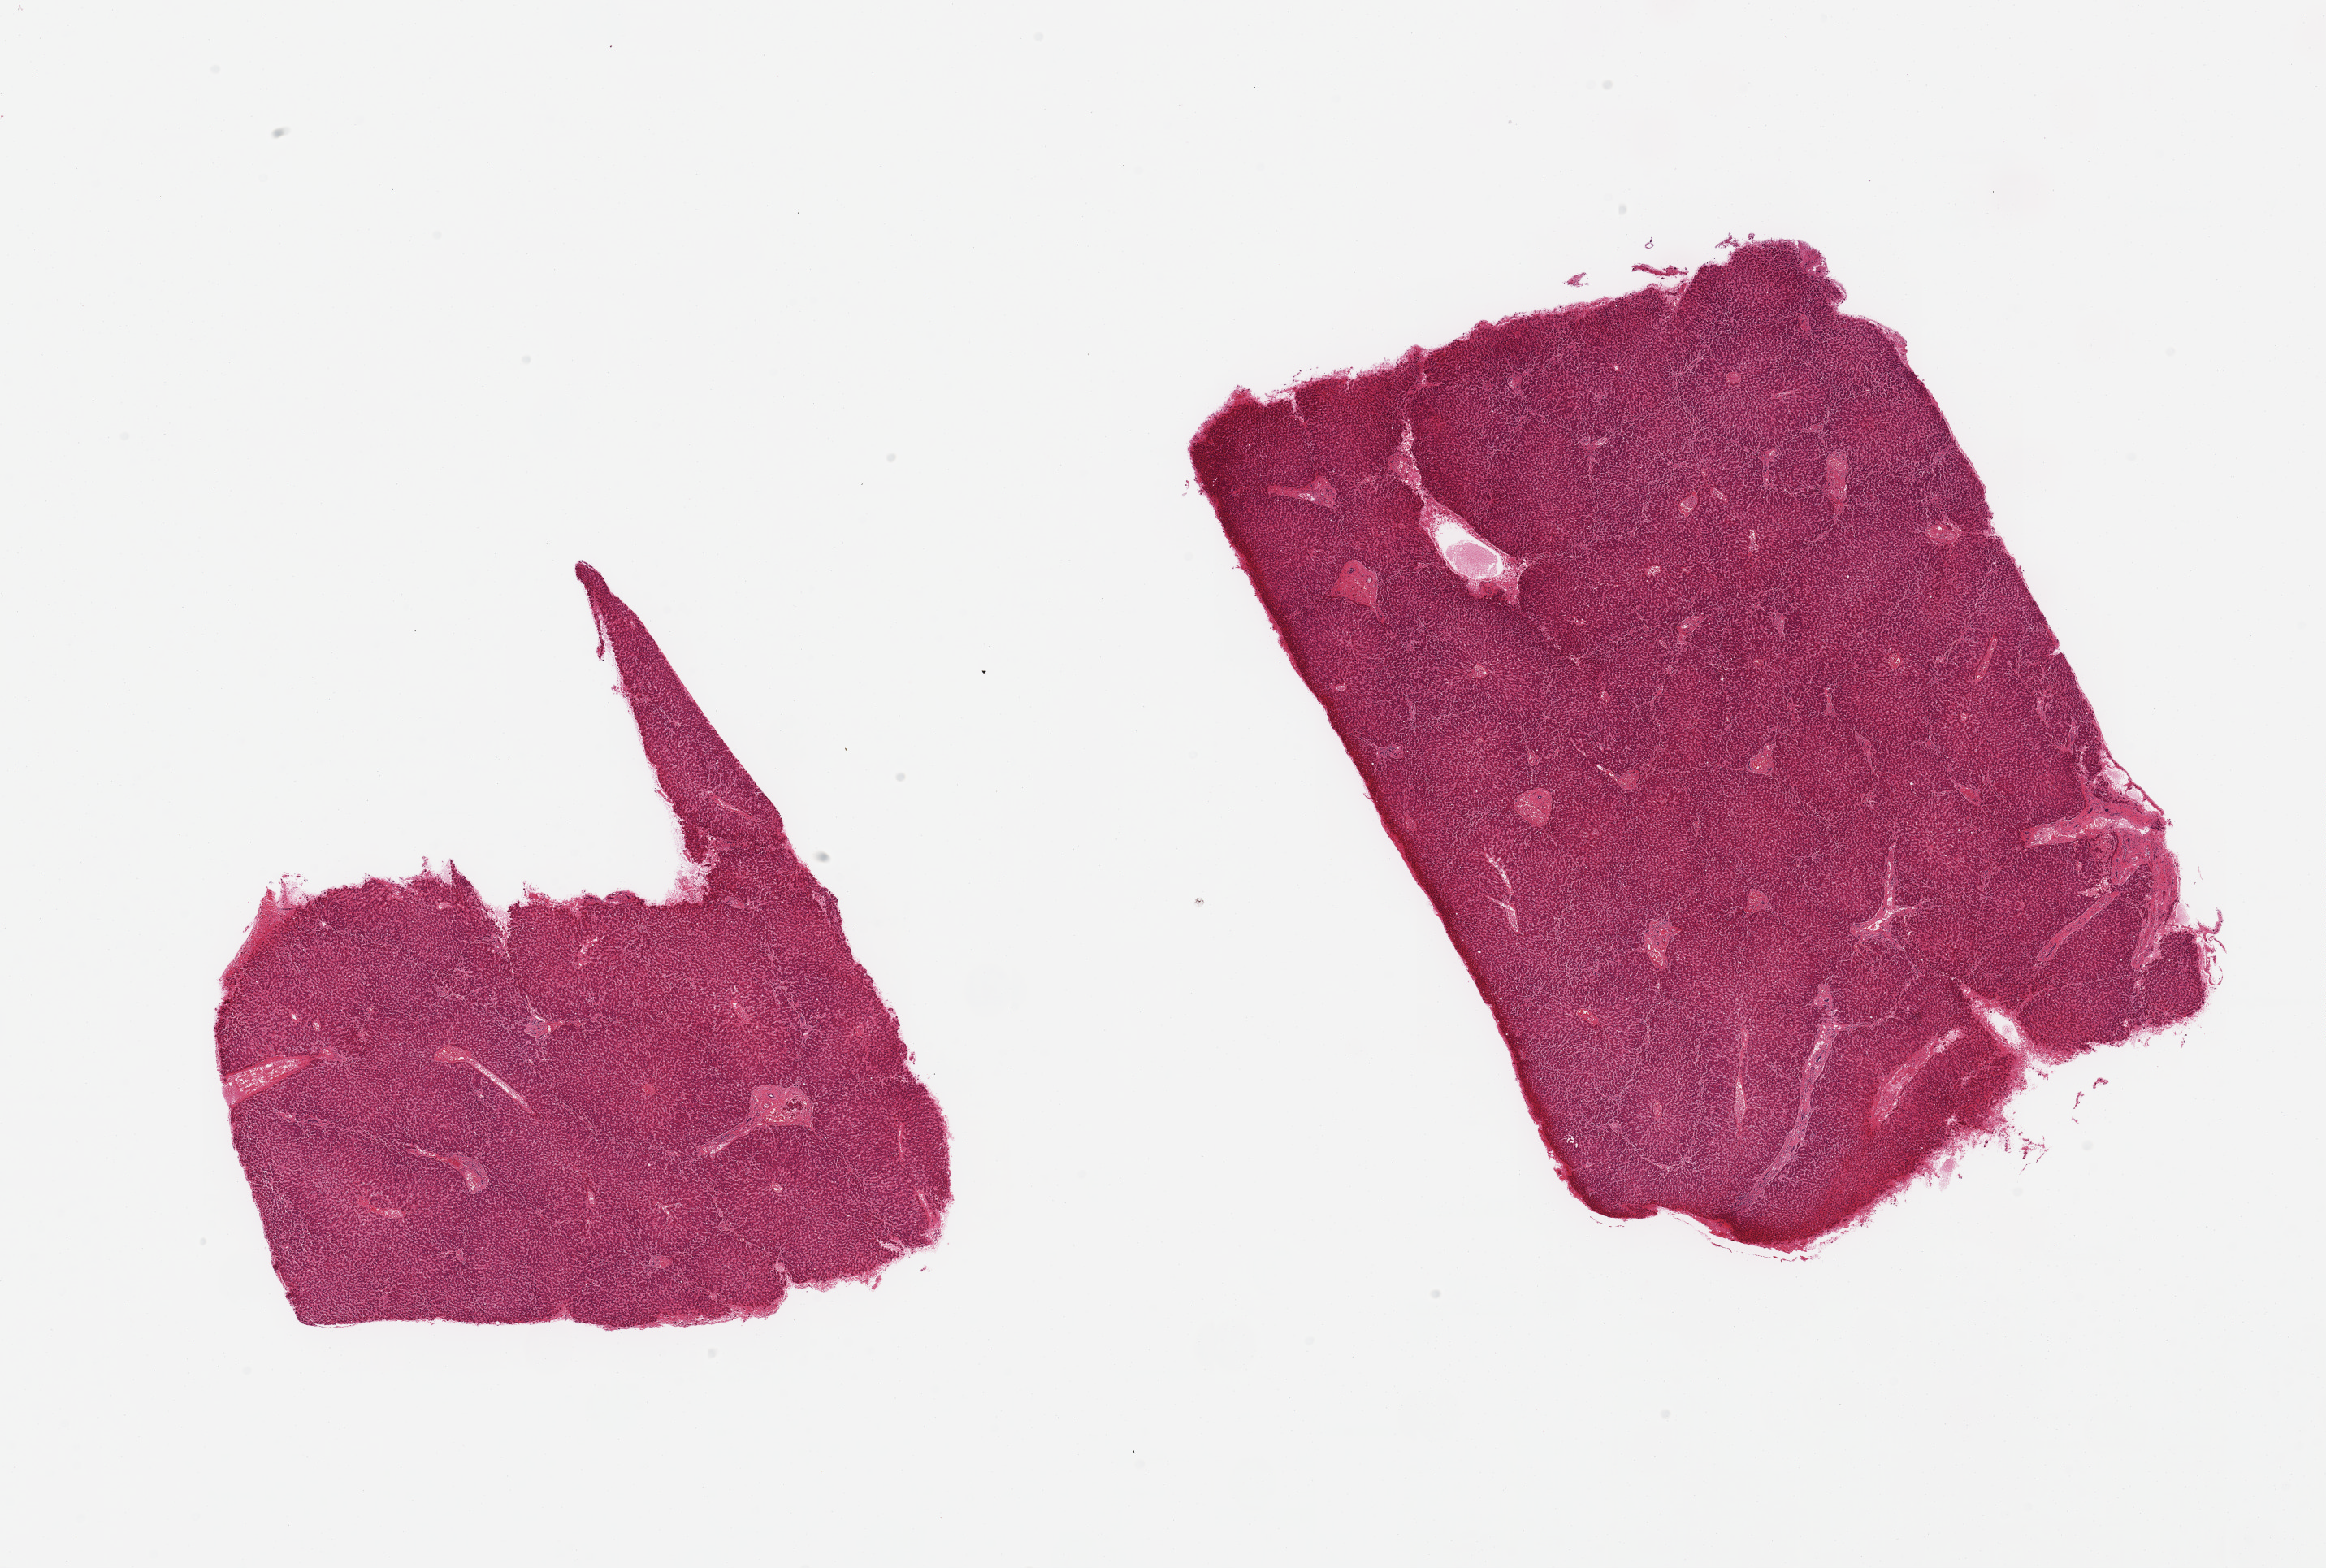
Whole-slide image, H&E stain — low-resolution overview of the scanned area, about 22.6 x 15.3 mm (slide scanned at 20x), PAXgene-fixed paraffin-embedded (PFPE) section, sampled site (target tissue): liver, tissue donor sample. Donor: female.
Reviewer comment on this tissue sample: 2 pieces; no infiltrates, fibrosis, congestion or fat.